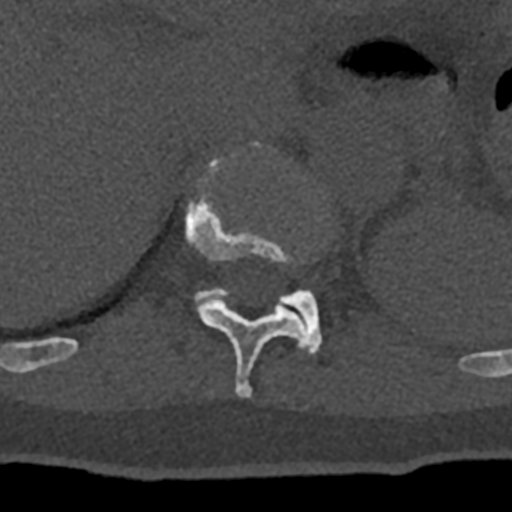
CT including the spine, one axial slice; slice 530 of 797 in the series (ordered by position); bone window (W 1800 / L 400 HU); 512 × 512 image matrix. Patient: male, 74 years. Case-level facts recorded for this patient, not image findings: primary cancer: renal; vertebrae with lytic lesions (as recorded): T10, L1, L2, L3, L4, L5.
Structures marked on this image (semi-automatic segmentation, software-assisted and operator-edited):
- T11 vertebra: bounding box (x1, y1, x2, y2) in pixels: (70, 141, 308, 398)
- T12 vertebra: (194, 288, 322, 354)